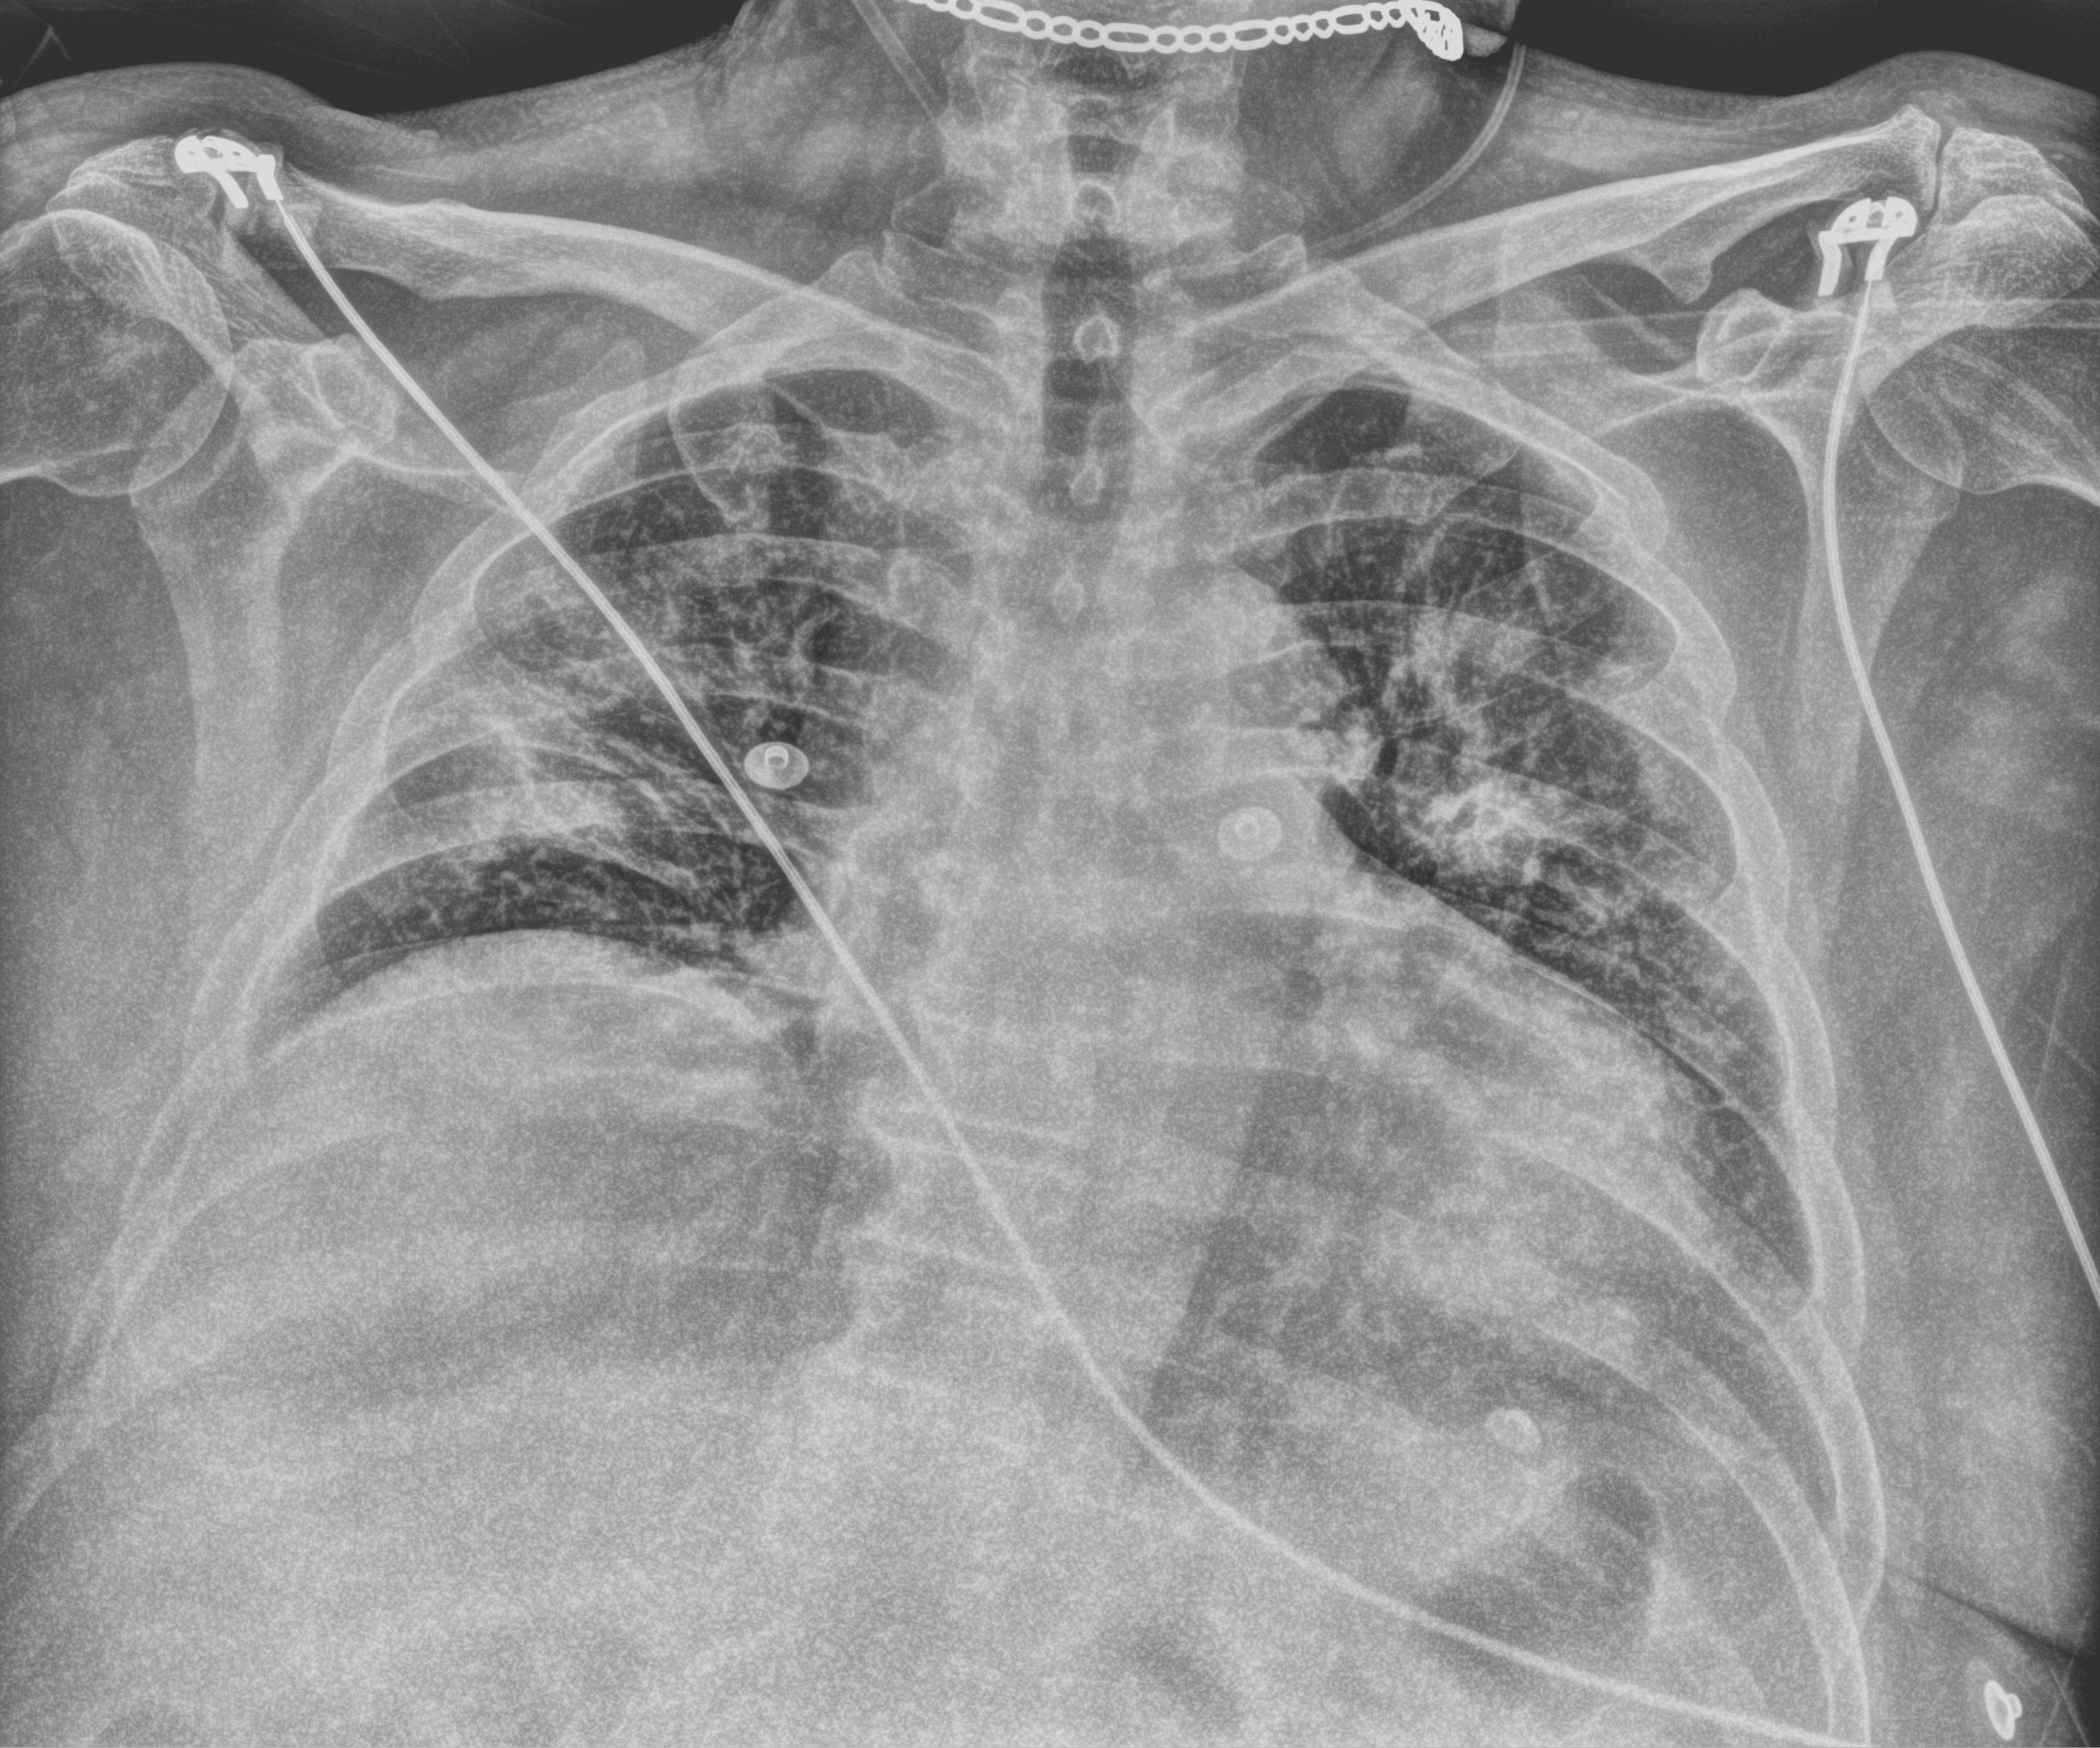
Portable chest radiograph; anteroposterior (AP) projection. Patient hospitalised with COVID-19; male, aged 60–74 years.
From the hospital-stay record, not from the radiograph (when in the stay this image was taken is not recorded):
- mechanically ventilated during this hospital stay: no
- length of hospital stay: 5 days